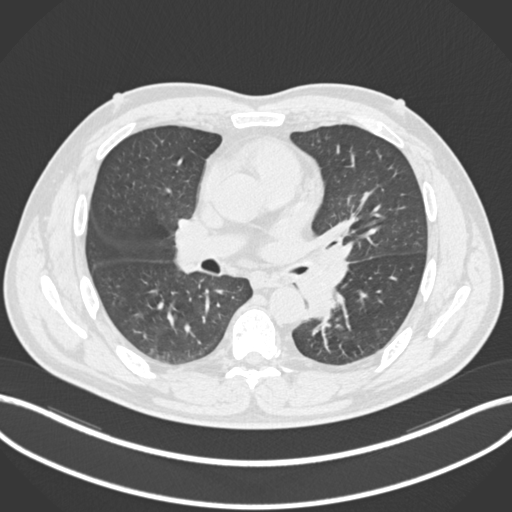
Chest CT, one axial slice. Position 123 of 223 along the scan axis. 120 kVp. Lung window (W 1500 / L -600 HU). 512 × 512 image matrix. Male patient, age 50 years. From the clinical record (not read from this slice): clinical TNM (as recorded): T2a N3 M0.
Annotated regions visible in this slice (bounding box drawn by a radiologist):
- lung tumour (recorded histology: squamous cell carcinoma): bounding box (x1, y1, x2, y2) in pixels: (297, 238, 357, 319)